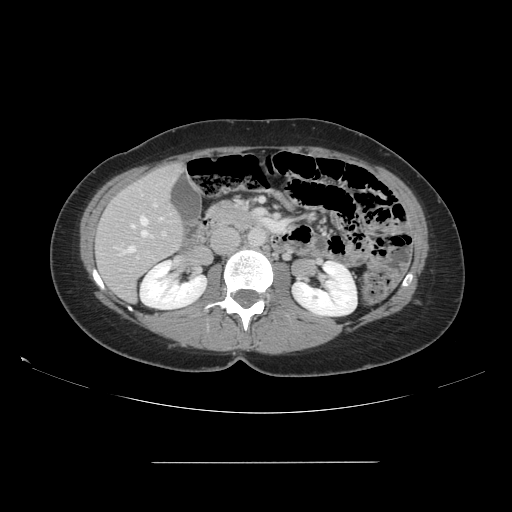
Contrast-enhanced abdominal CT, one axial slice; position 66 of 151 along the scan axis; intravenous contrast given; soft-tissue window (W 400 / L 40 HU); 512 × 512 image matrix, field of view 421 × 421 mm. Female patient, age 46 years. From the clinical record (not read from this slice): diagnosis: colorectal cancer liver metastases, imaged before liver resection; multiple liver metastases: yes; largest metastasis: 3 cm; disease in both lobes: yes.
Annotated regions visible in this slice (outlined manually by an expert reader):
- hepatic veins: bounding box [x1, y1, x2, y2] px = [124, 216, 163, 253]
- liver: [97, 164, 184, 301]
- planned liver remnant (the part of the liver to remain after resection): [97, 164, 184, 301]
- portal vein (with intrahepatic branches): [136, 202, 167, 260]